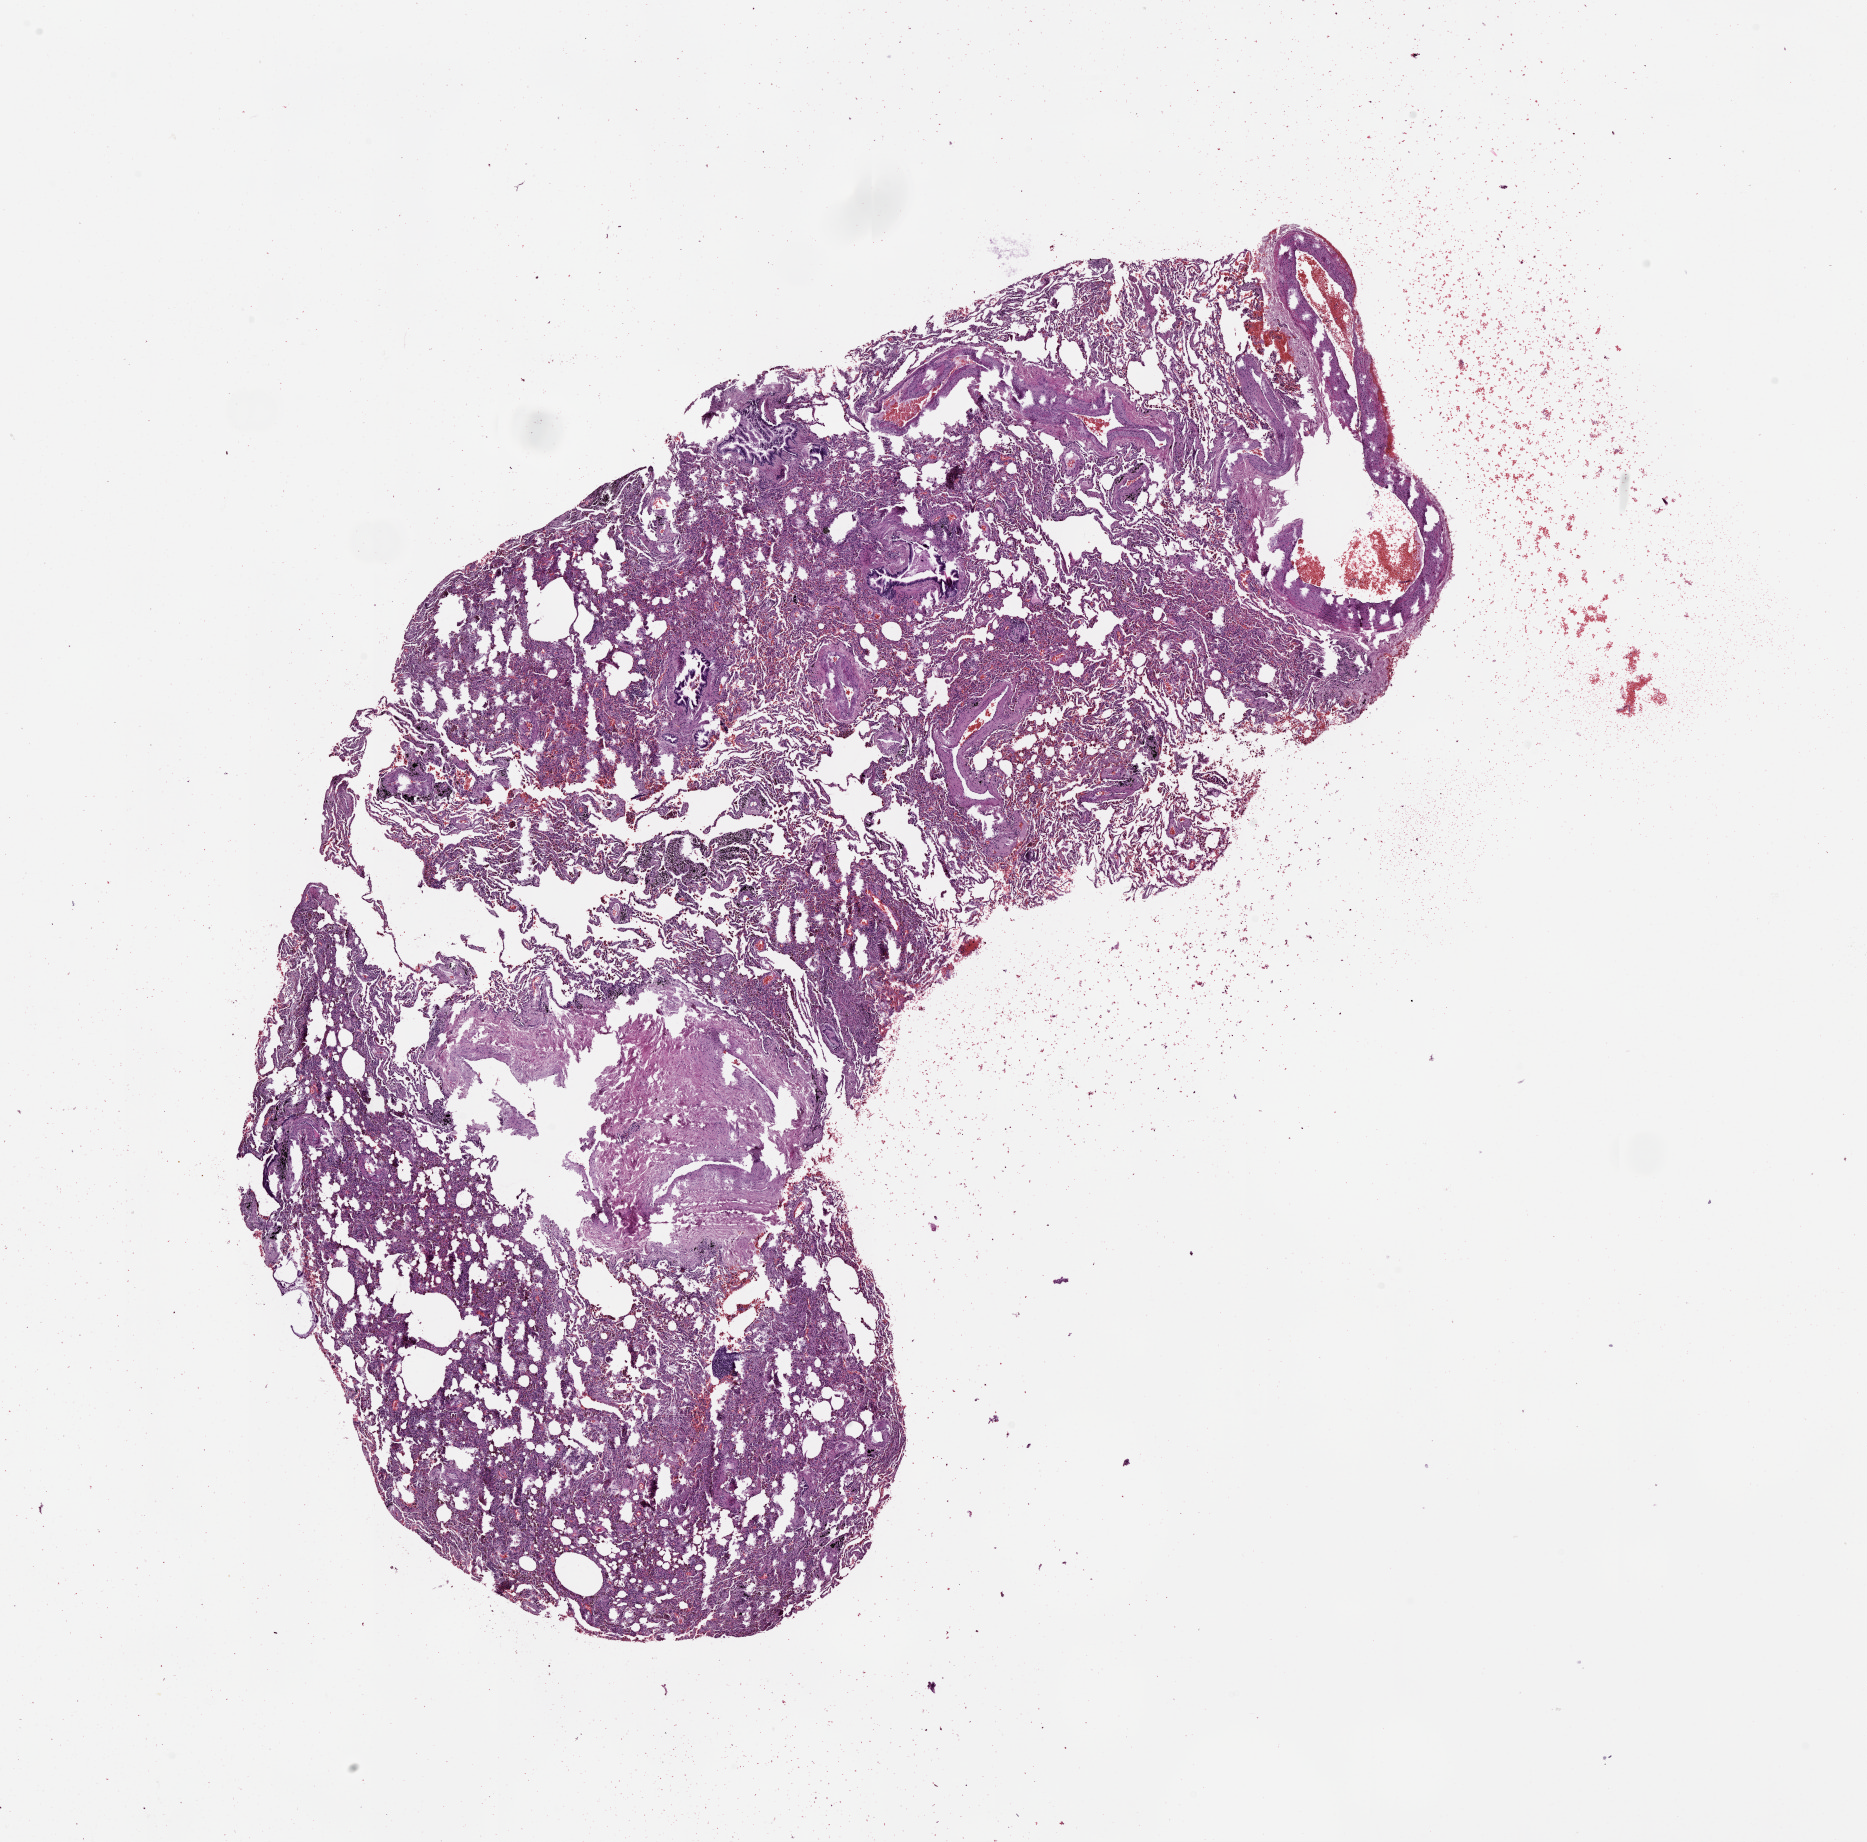
Whole-slide histology image, Hematoxylin and eosin (H&E) stained — whole scanned area (about 15.0 x 14.8 mm) shown as a low-resolution overview. Normal (non-tumour) tissue sample, lung. Male, 59 y/o.
- this section: normal (non-tumour) tissue from the same patient
- patient diagnosis (cohort enrolment): squamous cell carcinoma (lung)